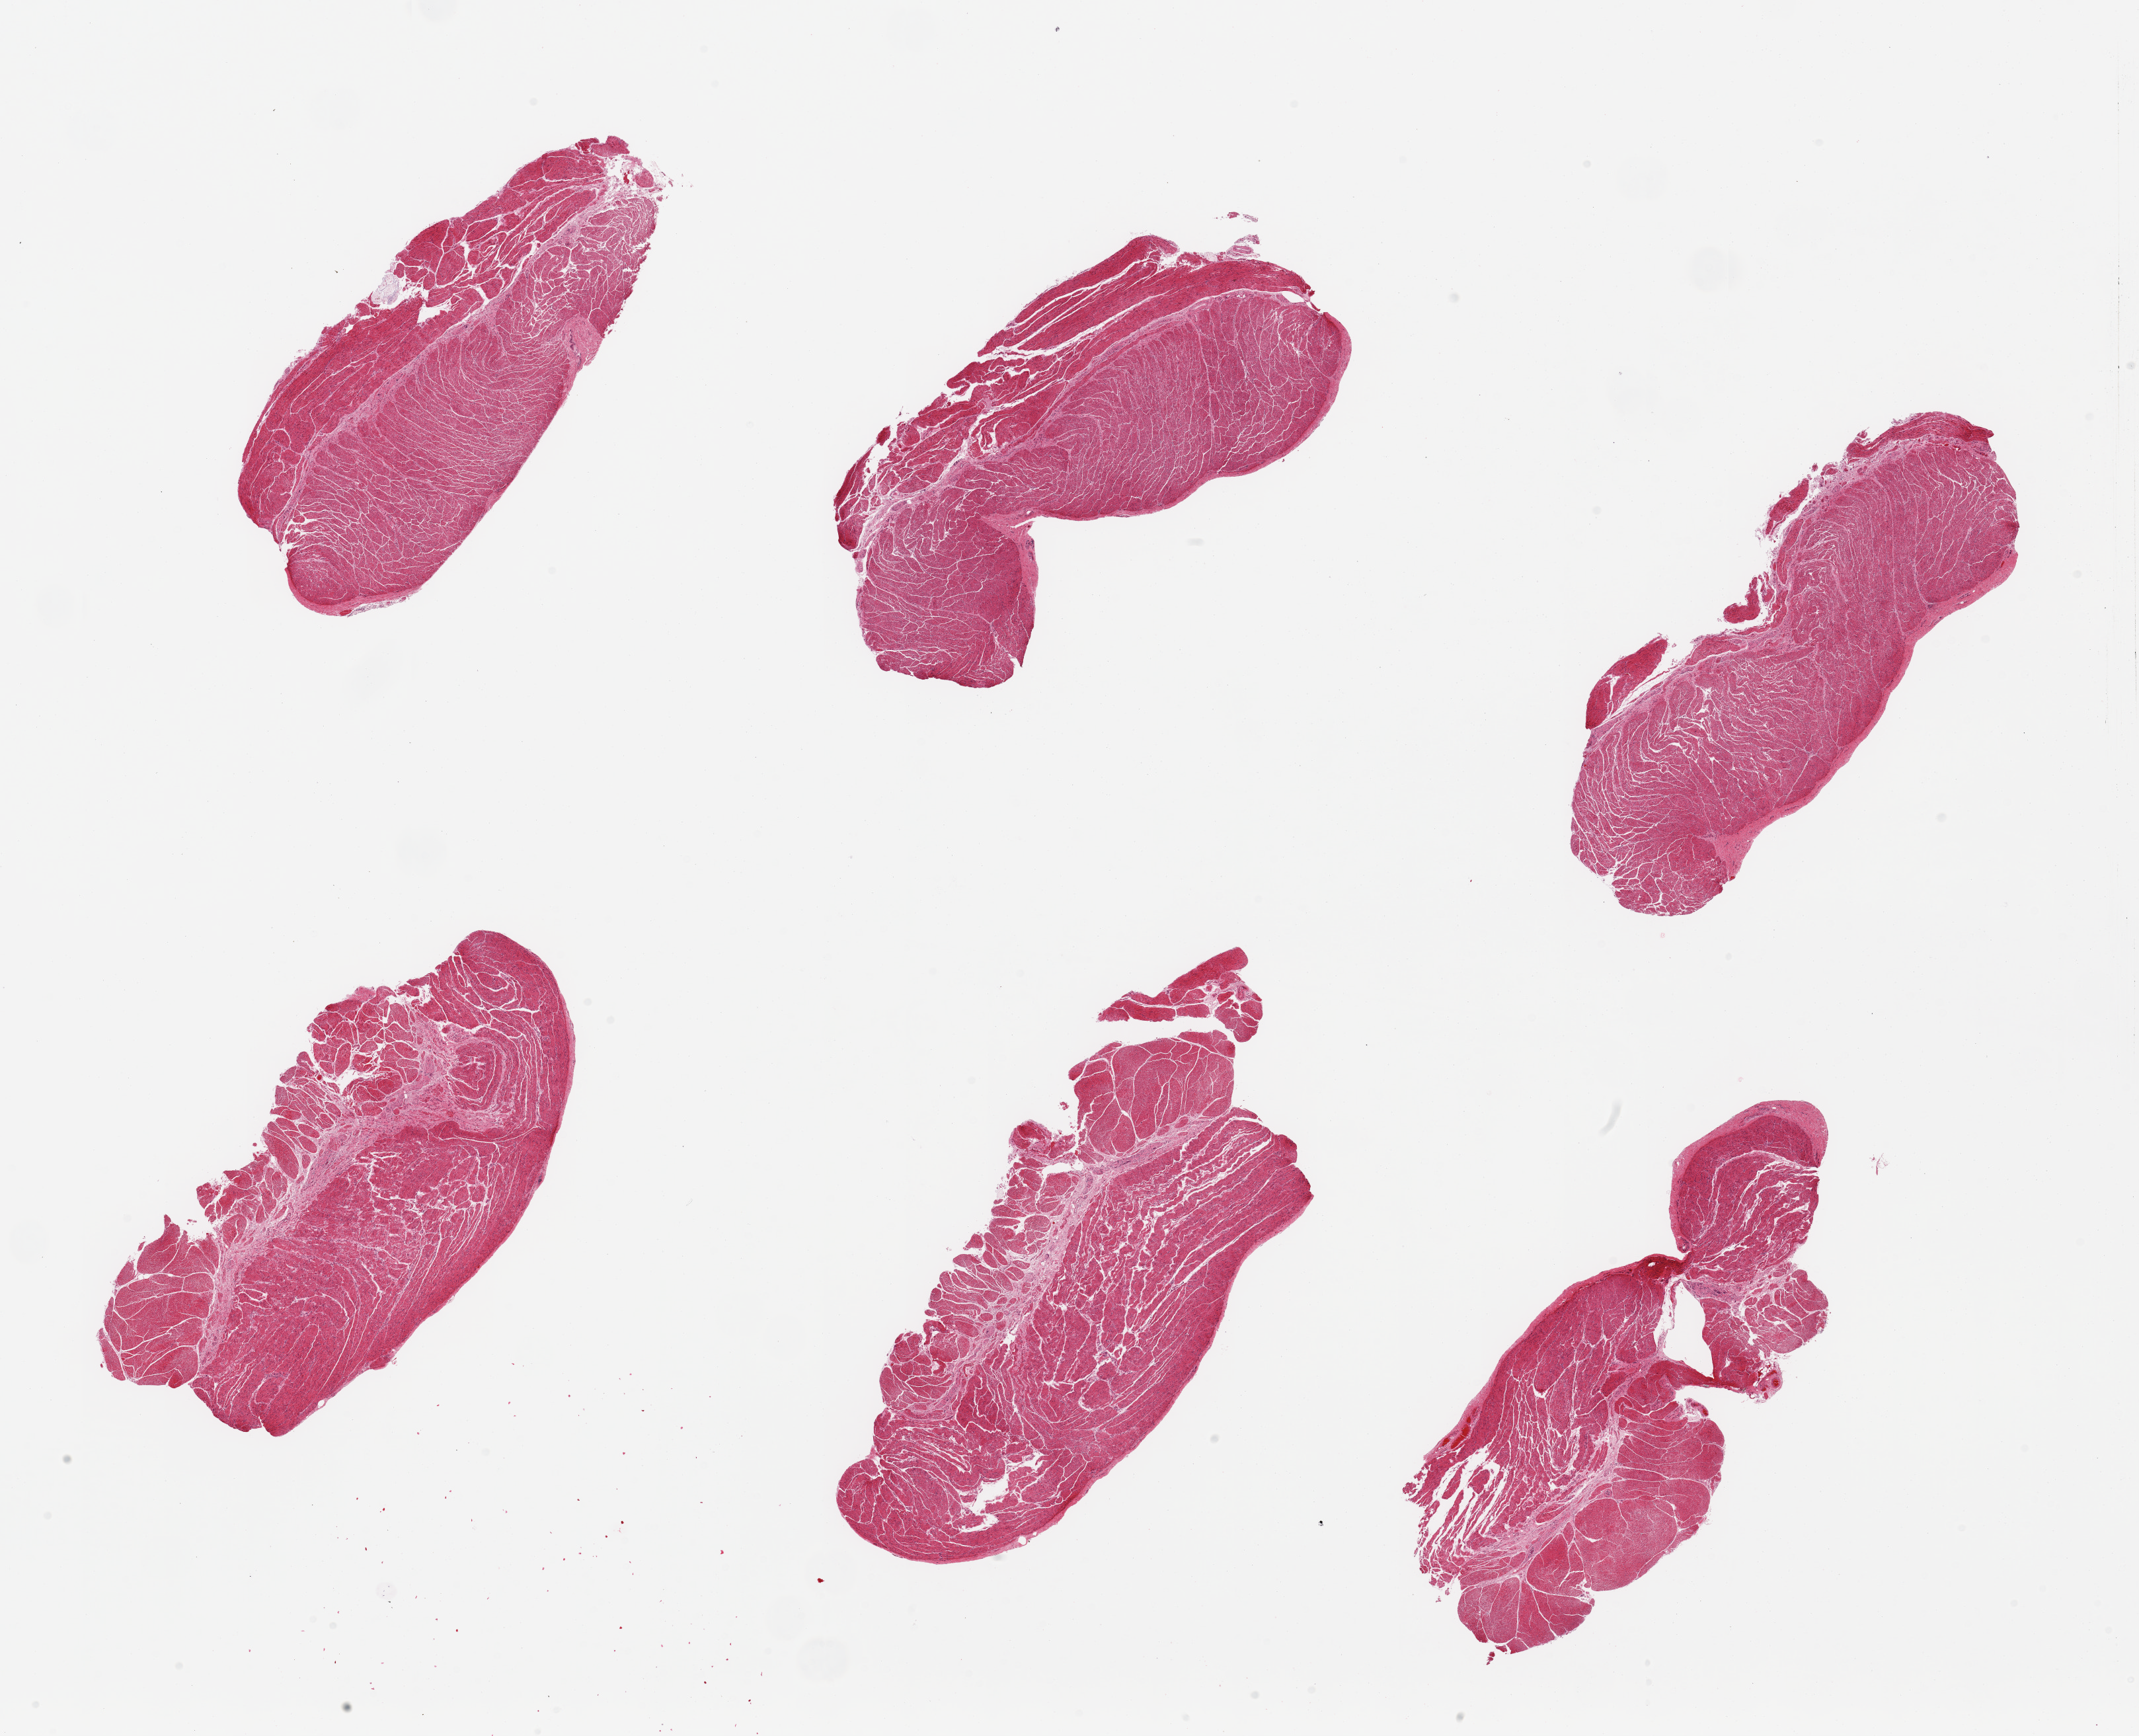
Digitized haematoxylin and eosin-stained section, low-resolution overview of the scanned area, about 25.6 x 20.8 mm. PAXgene-fixed paraffin-embedded (PFPE) section. Target tissue: esophageal muscle. Tissue donor sample. Donor sex: male.
Review note (as recorded): 6 pieces, target muscularis, good specimens.